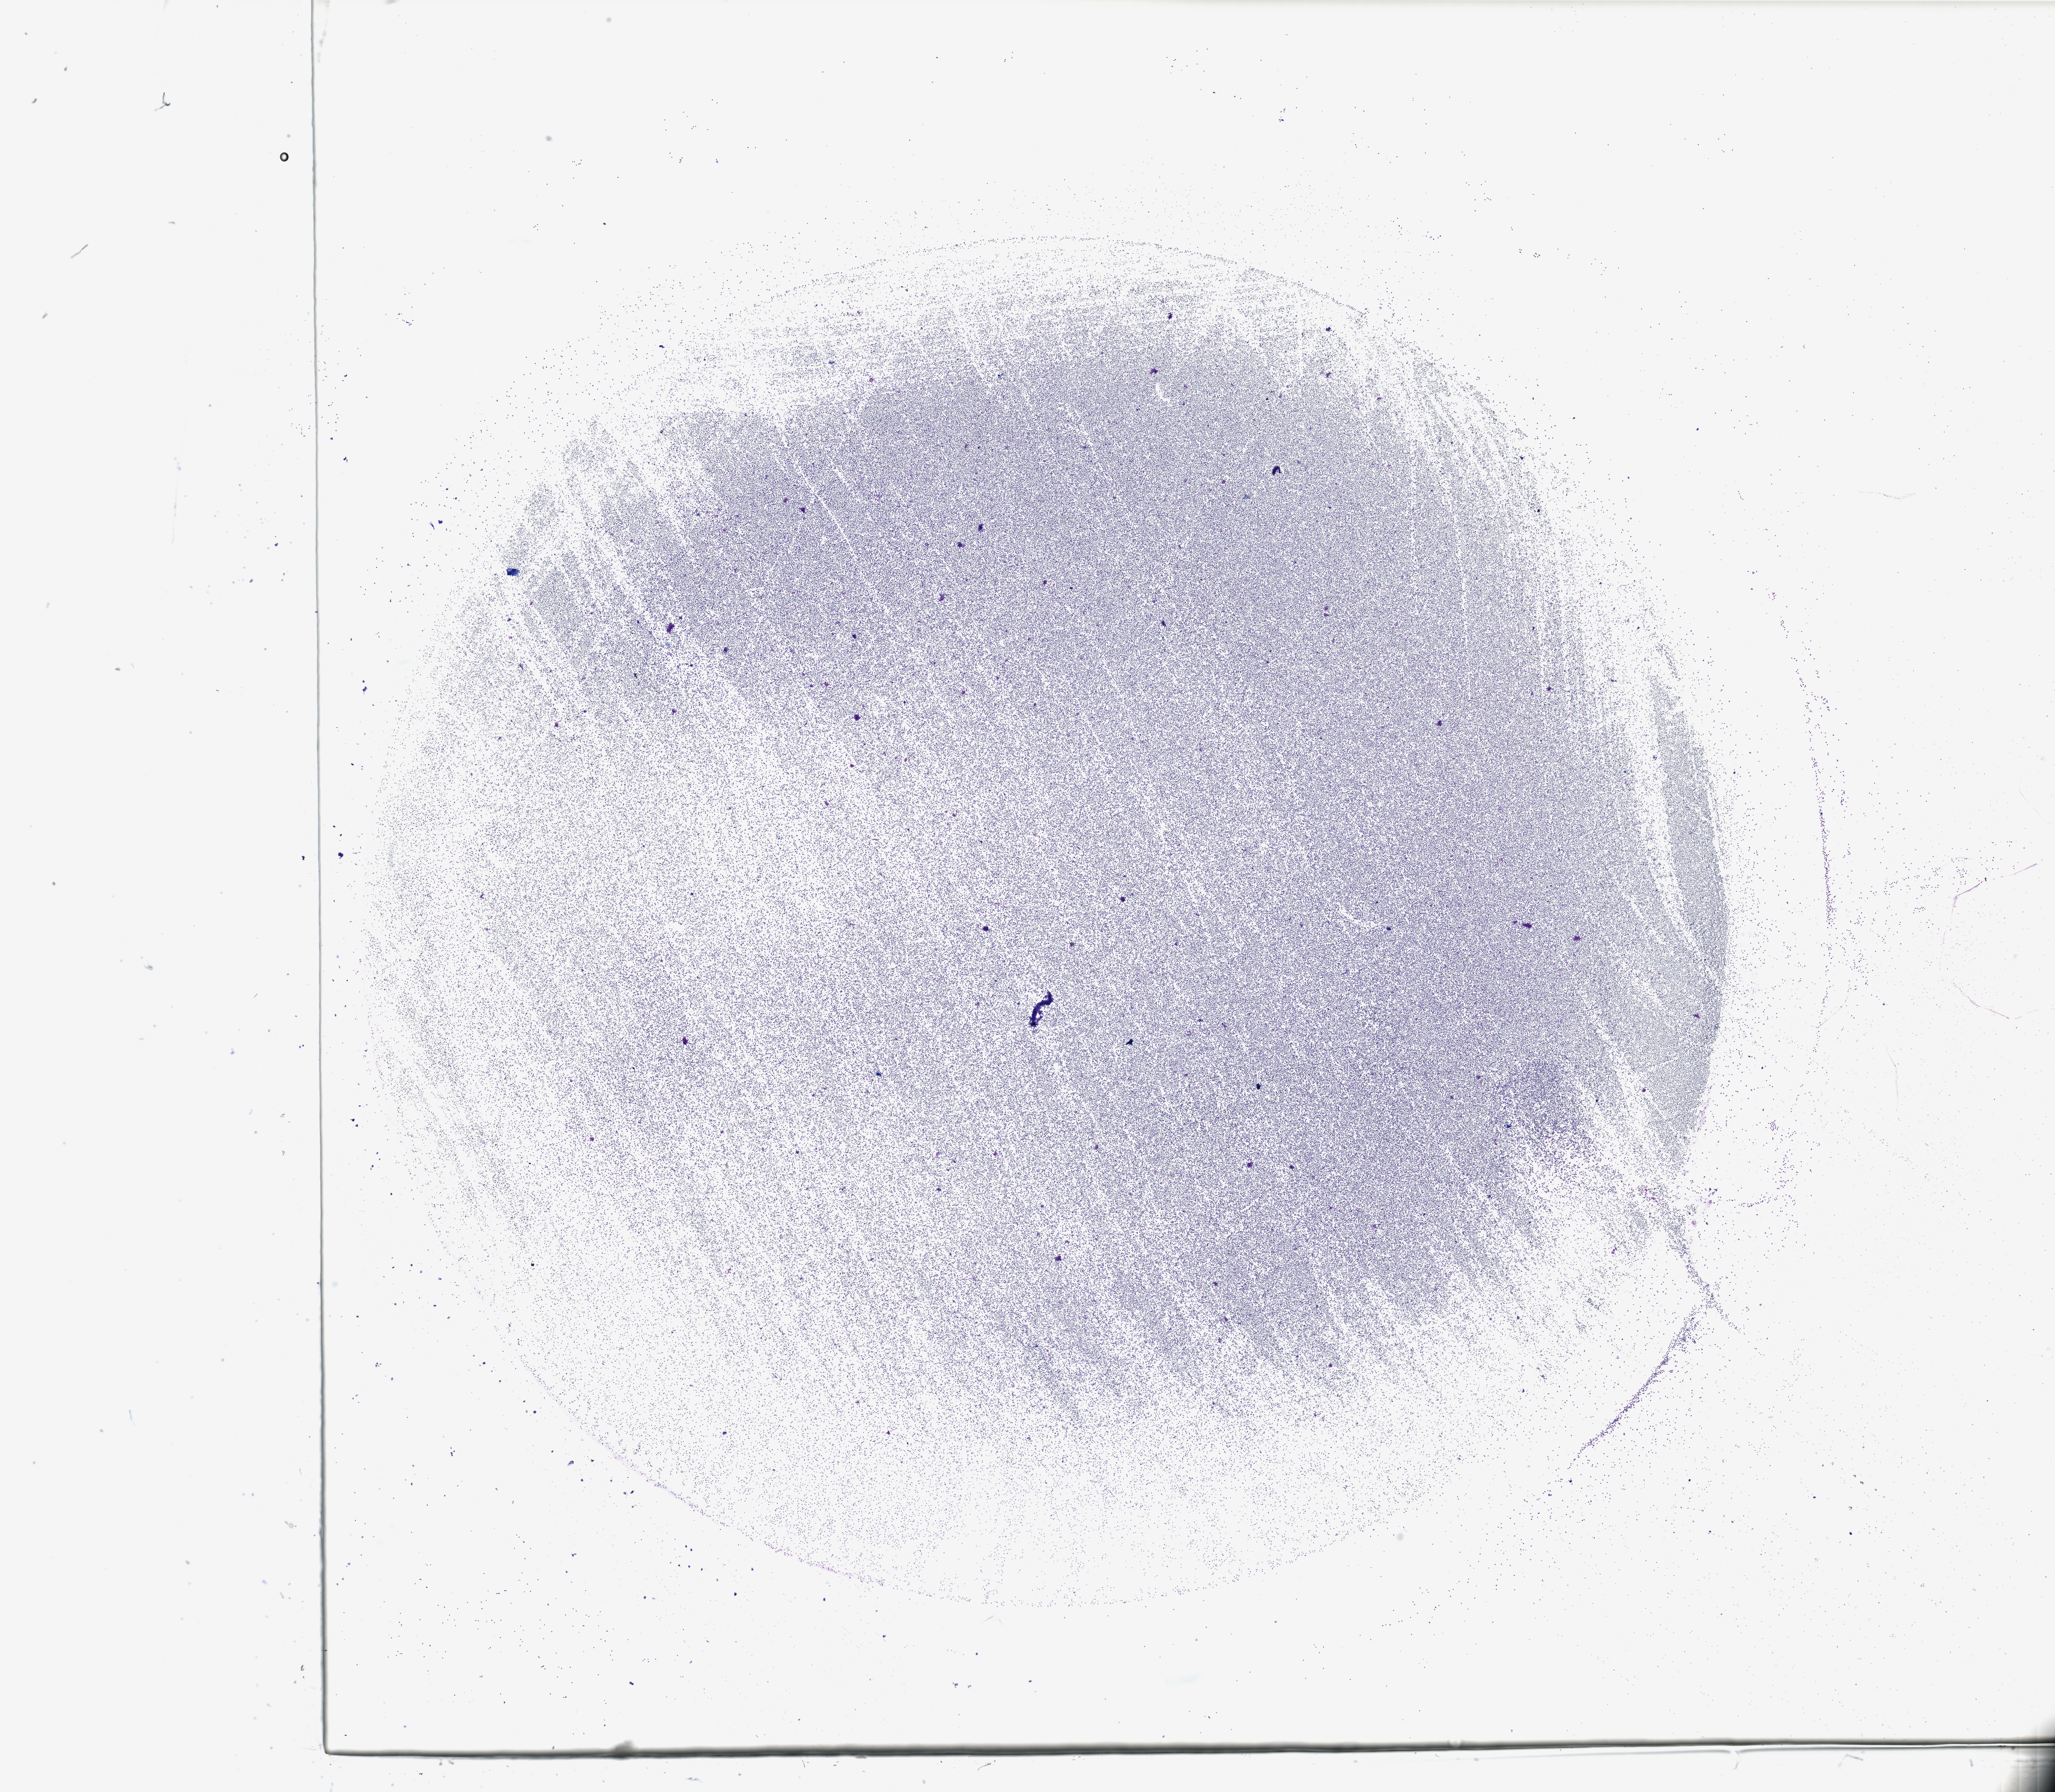
Whole-slide histology image, Hematoxylin and eosin (H&E) stained — whole scanned area (about 27.0 x 23.6 mm, slide scanned at 40x) shown as a low-resolution overview. Bone marrow (leukaemic) sample. Patient: female, age 69 years. Blasts: 99%.
WHO classification: Acute monoblastic and monocytic leukemia. Diagnosis: Acute Myeloid Leukemia. FAB classification: M5.